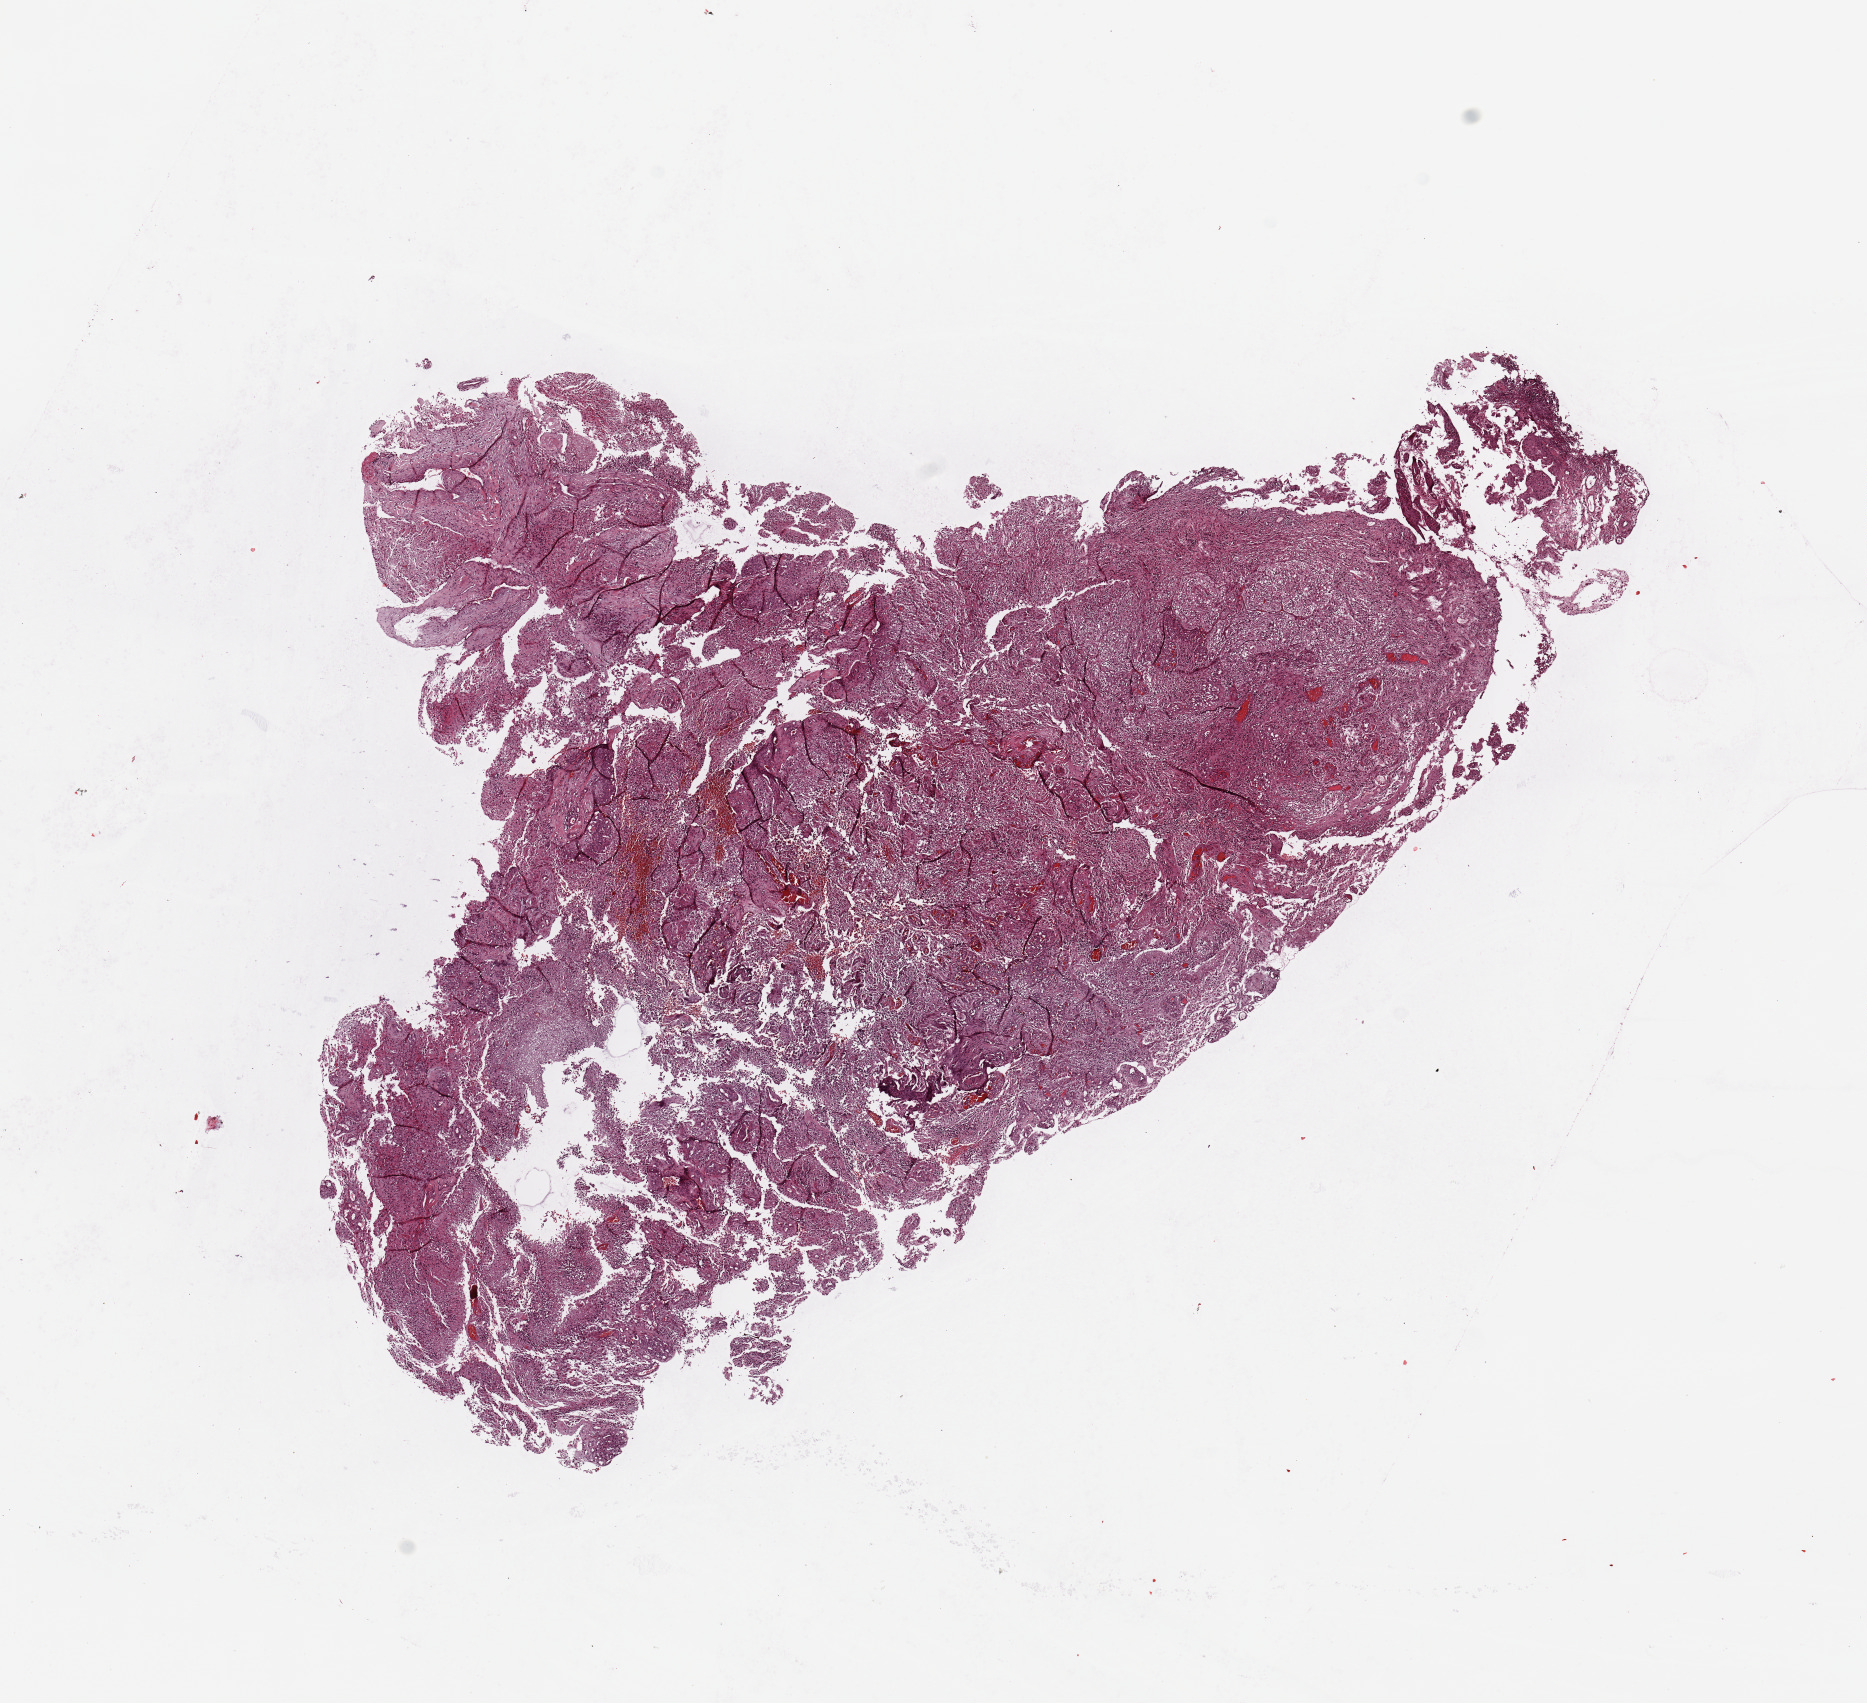
Hematoxylin and eosin (H&E) stained whole-slide image — shown as a low-resolution overview of the whole scanned area (about 14.8 x 13.5 mm, acquisition: 20x scan), brain, tumour tissue. 59-year-old male patient.
Primary tumour site (as recorded): temporal lobe. Histologic diagnosis: Glioblastoma.